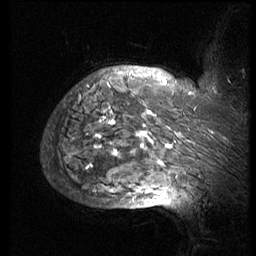
Breast MRI (dynamic contrast-enhanced), one sagittal slice. Position 60 of 74 along the scan axis. 3 images stored at this slice position (order not interpretable as contrast timing). 1.5 T. TE 4.2 ms, TR 8.9 ms. 256 × 256 image matrix, field of view 200 × 200 mm. Patient: female, 57 years. From the clinical record (not read from this slice): setting: breast cancer imaged before/during neoadjuvant chemotherapy; receptor status: HER2-positive.
Structures marked on this image (semi-automatic segmentation, software-assisted and operator-edited):
- analysis volume of interest (the breast-tissue region the enhancement analysis was run in; not a lesion): bounding box (x1, y1, x2, y2) in pixels: (51, 67, 248, 173)
- tumour enhancement mask (voxels above the 140 % enhancement threshold inside the analysis volume of interest): (74, 80, 213, 169)